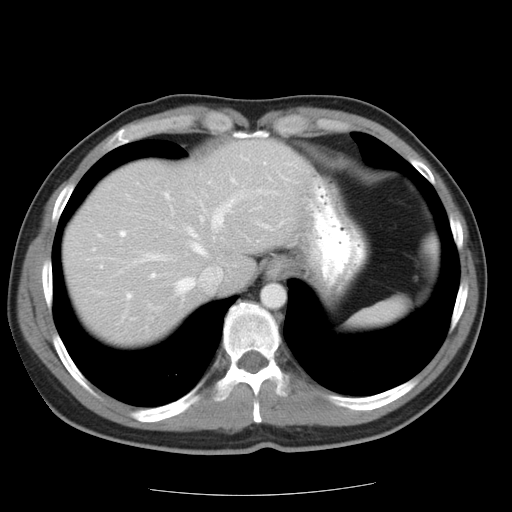
Contrast-enhanced abdominal CT, one axial slice; slice 18 of 22 in the series (ordered by position); soft-tissue window (W 400 / L 40 HU); 7.5 mm slice thickness; 512 × 512 image matrix, field of view 359 × 359 mm. Male patient, age 41 years. From the clinical record (not read from this slice): diagnosis: colorectal cancer liver metastases, imaged before liver resection; multiple liver metastases: no; largest metastasis: 2.7 cm.
Annotated regions visible in this slice (expert manual segmentation):
- hepatic veins: box from (x=143, y=201) to (x=235, y=293) px
- liver: (x=65, y=141)–(x=301, y=342)
- planned liver remnant (the part of the liver to remain after resection): (x=65, y=141)–(x=300, y=328)
- portal vein (with intrahepatic branches): (x=121, y=180)–(x=268, y=299)